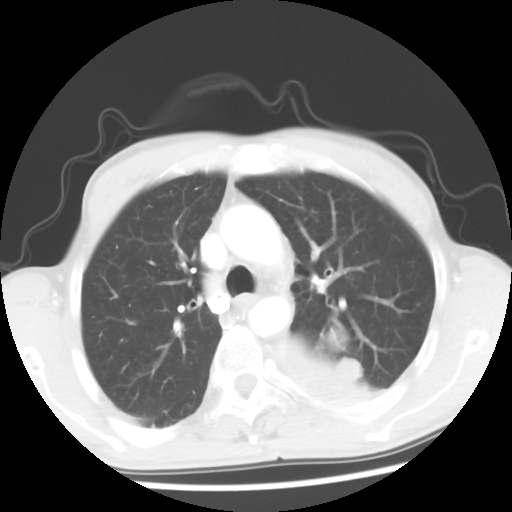
Chest CT, one axial slice. Reconstruction kernel STANDARD. Lung window (W 1500 / L -600 HU). 5 mm slice thickness. 512 × 512 image matrix, field of view 318 × 318 mm. Male patient, age 60 years. Case-level facts recorded for this patient, not image findings: clinical TNM (as recorded): T4 N0 M0.
Structures marked on this image (rectangle marked by the reading radiologist):
- lung tumour (recorded histology: squamous cell carcinoma): box from (x=278, y=331) to (x=375, y=415) px